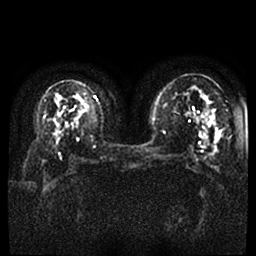
Breast MRI, one axial slice. Position 18 of 45 along the scan axis. Diffusion-weighted series; image 2 of 4 stored at this slice position (different b-values; order by instance number). 1.5 T. 256 × 256 image matrix, field of view 340 × 340 mm. Female patient.
Annotated regions visible in this slice (manually delineated by an expert):
- tumour on diffusion-weighted imaging: box from (x=208, y=146) to (x=218, y=171) px